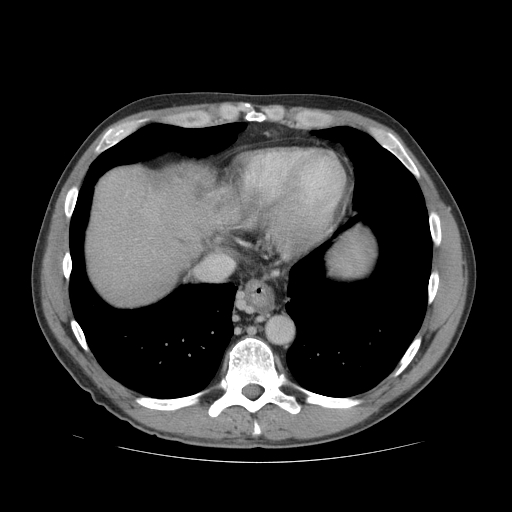
Contrast-enhanced abdominal CT (liver protocol), one axial slice. Slice 69 of 81 in the series (ordered by position). Soft-tissue window (W 400 / L 40 HU). 512 × 512 image matrix, field of view 400 × 400 mm. Case-level facts recorded for this patient, not image findings: diagnosis: hepatocellular carcinoma (patient treated with transarterial chemoembolisation; whether this scan precedes or follows treatment is not stated here); TNM stage (as recorded): Stage-IVB; Child-Pugh class: B; tumour differentiation: well differentiated; tumour nodularity: multinodular.
Outlined on this slice (semi-automatic segmentation, software-assisted and operator-edited):
- liver parenchyma outside the tumour (the mass and vessels are separate outlines, so this box may not span the whole liver): bounding box (x1, y1, x2, y2) in pixels: (86, 164, 234, 304)
- mass: (98, 165, 146, 218)